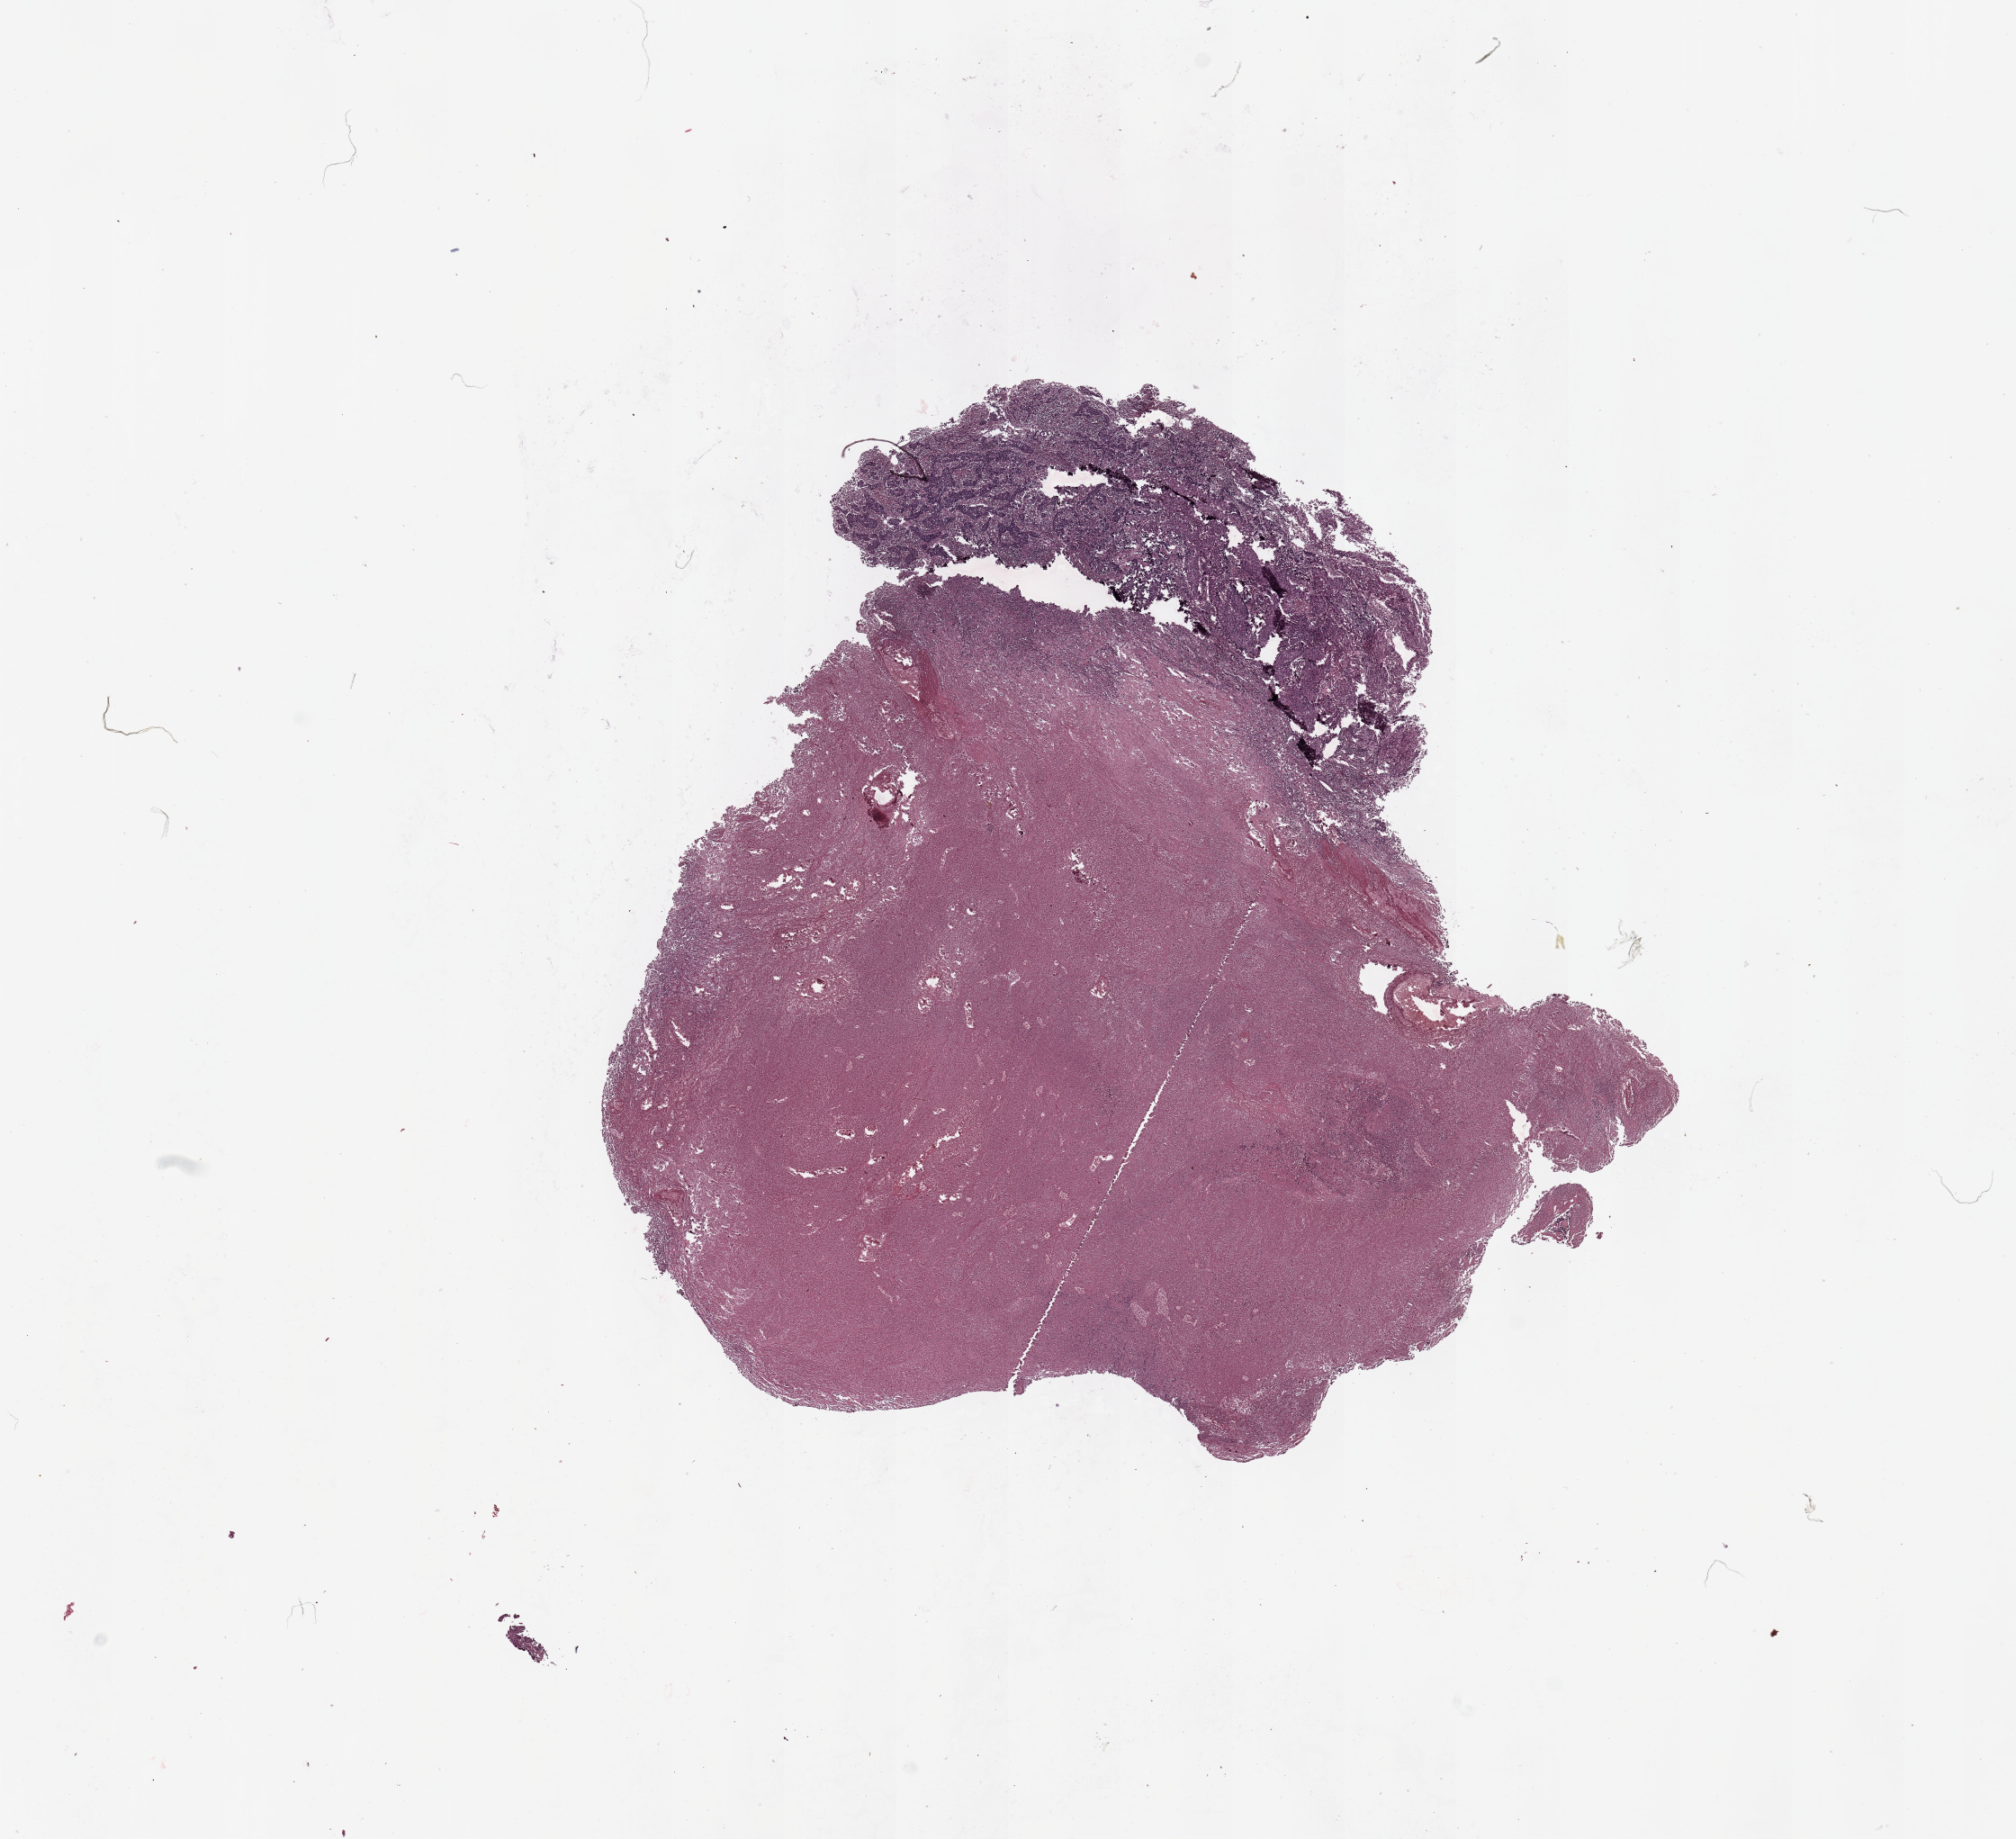
H&E-stained whole-slide image — shown as a low-resolution overview of the whole scanned area (about 17.7 x 16.2 mm, from a 20x scan); uterus, tumour tissue. Patient: female, age 58 years. Histologic grade: G3 (poorly differentiated).
• AJCC pathologic stage: III
• diagnosis: Endometrioid adenocarcinoma, NOS